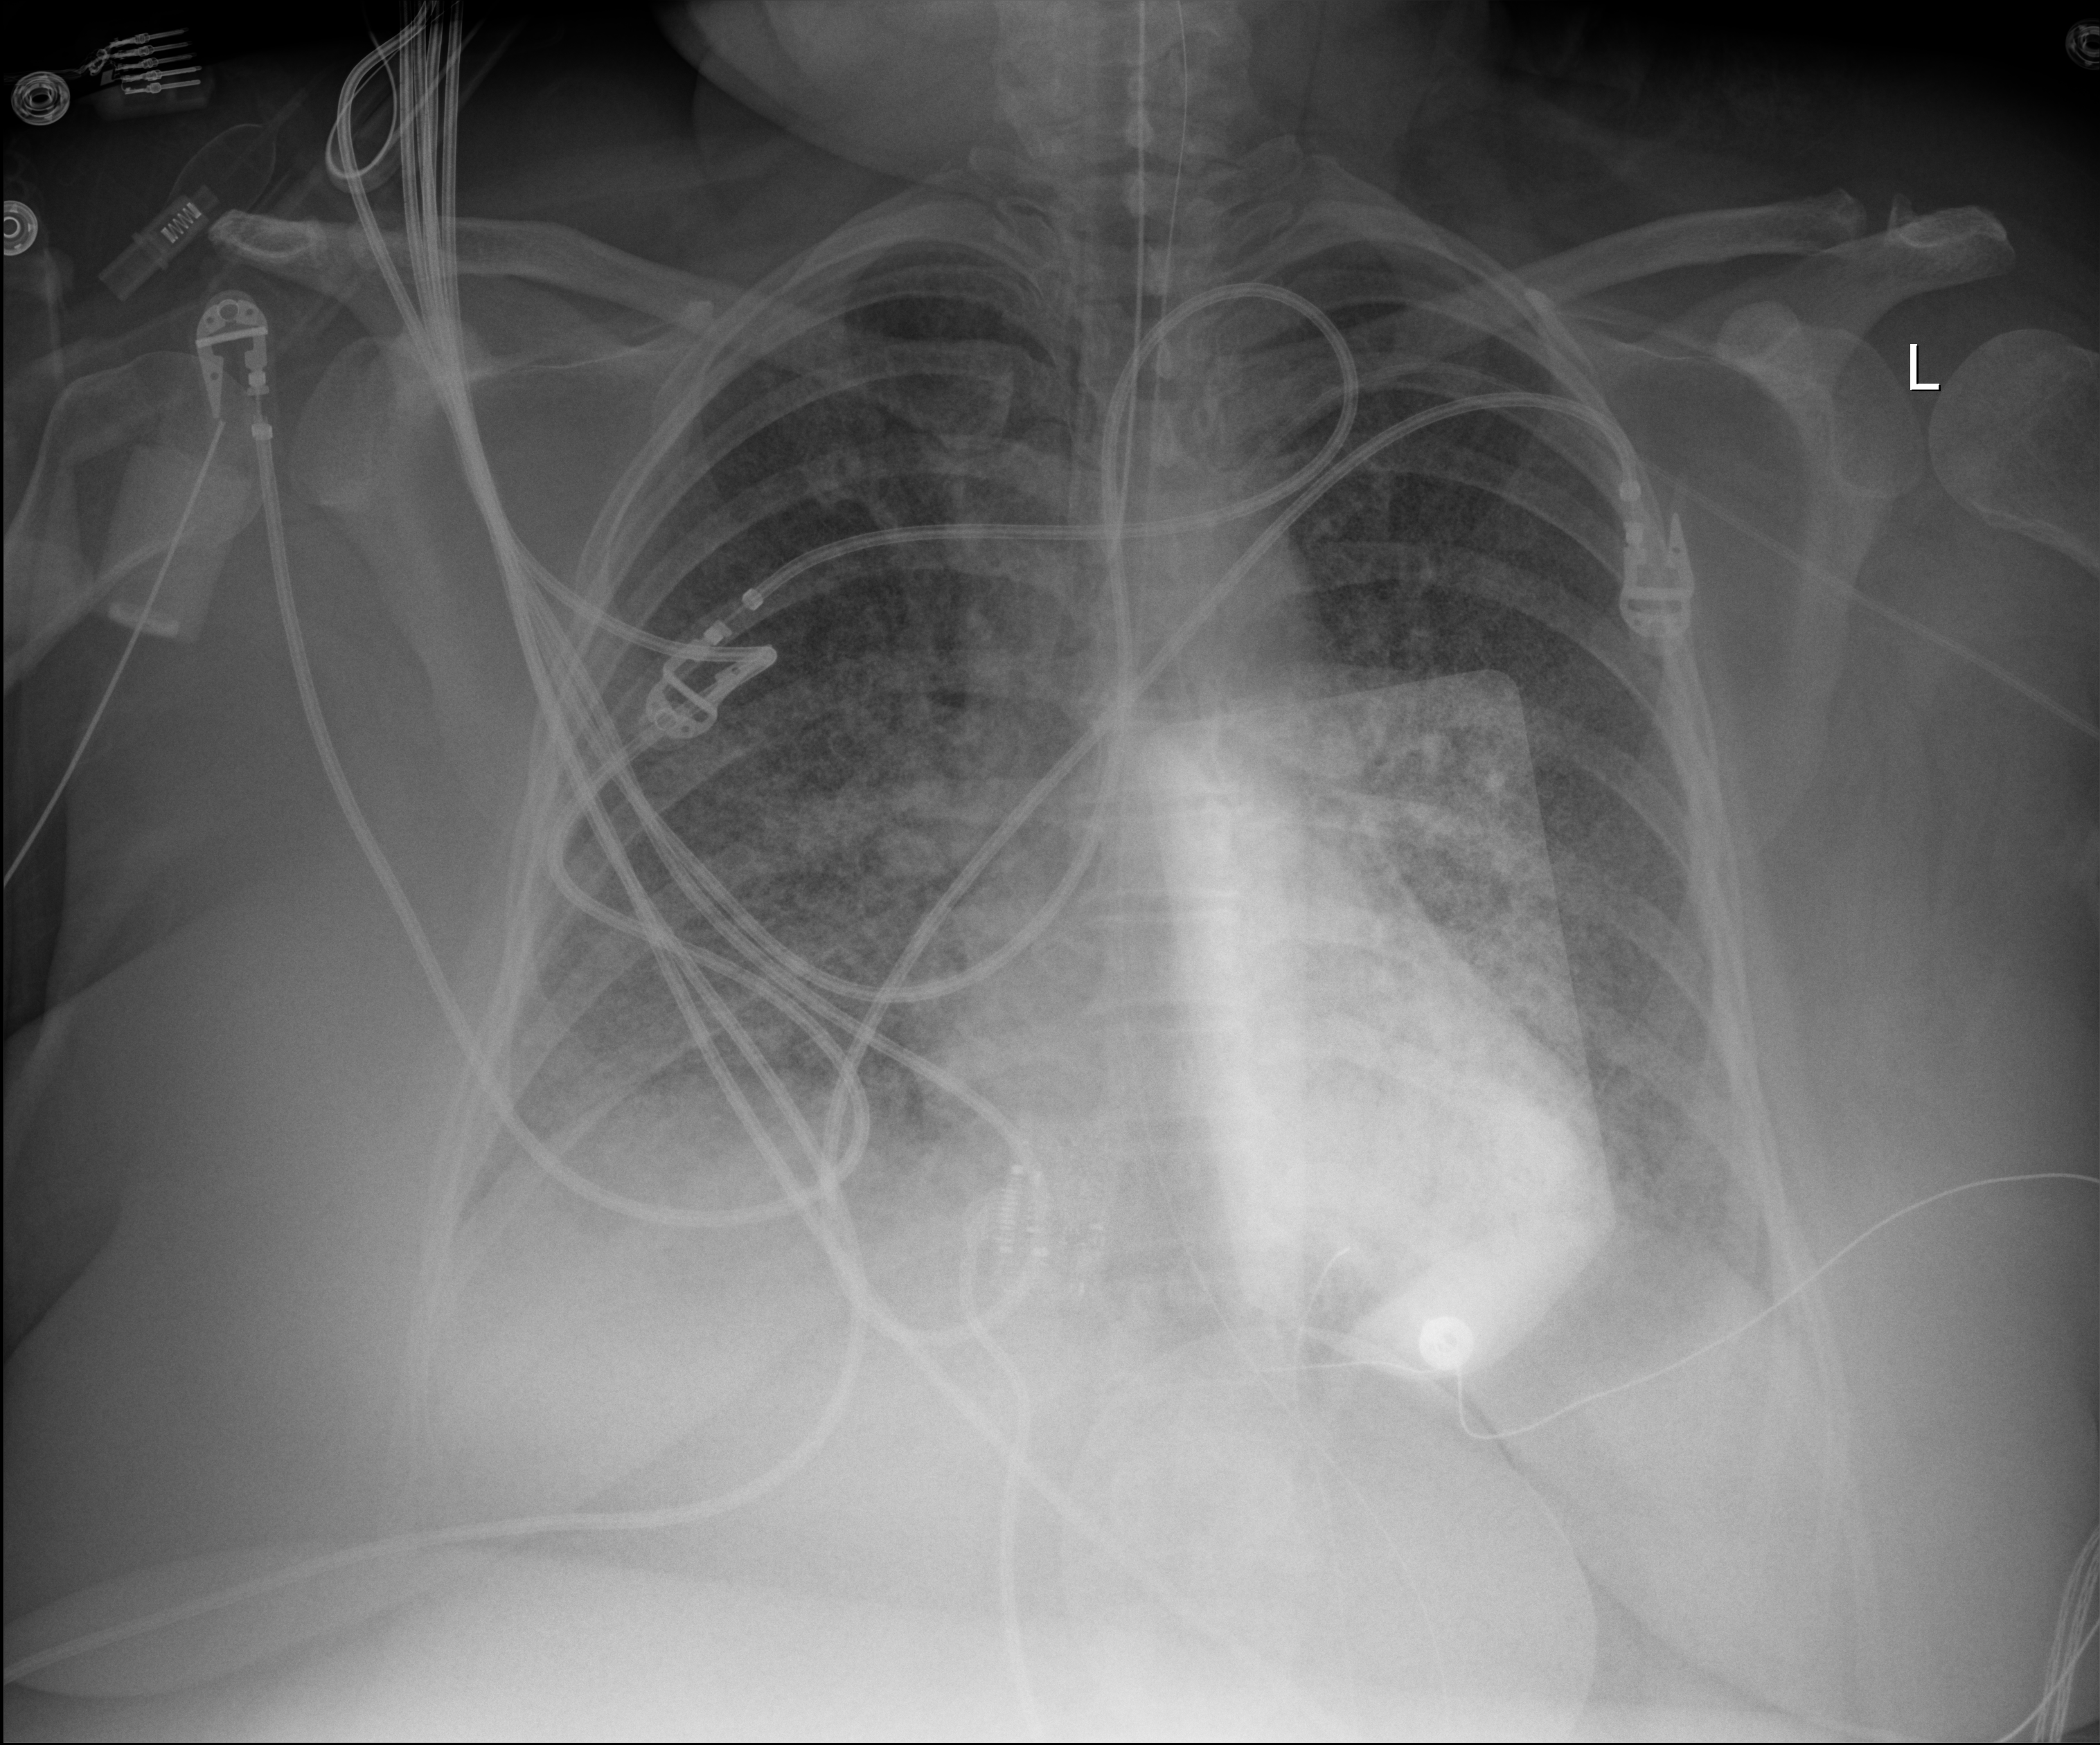
Bedside chest radiograph (digital radiography), anteroposterior (AP) projection. Patient hospitalised with COVID-19; female, aged 18–59 years.
Admission-level facts for this patient (not findings on this image; timing relative to this image not recorded):
- hypertension (admission record): yes
- admitted to intensive care during this hospital stay: yes
- length of hospital stay: 95 days